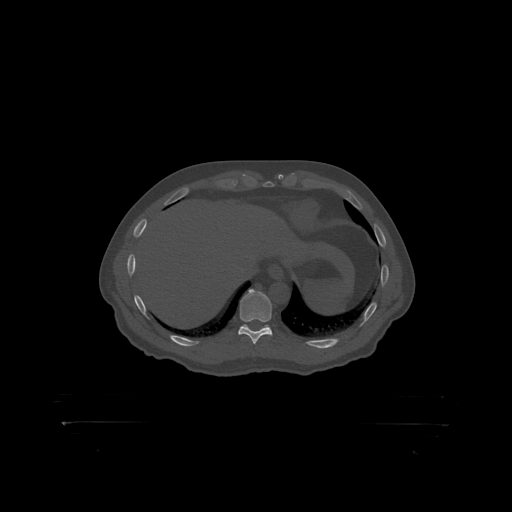
CT including the spine, one axial slice. Slice 397 of 399 in the series (ordered by position). Bone window (W 1800 / L 400 HU). 512 × 512 image matrix, field of view 650 × 650 mm. Patient: male, 46 years. From the clinical record (not read from this slice): primary cancer: skin.
Outlined on this slice (semi-automatic segmentation, software-assisted and operator-edited):
- T10 vertebra: box from (x=240, y=290) to (x=273, y=319) px